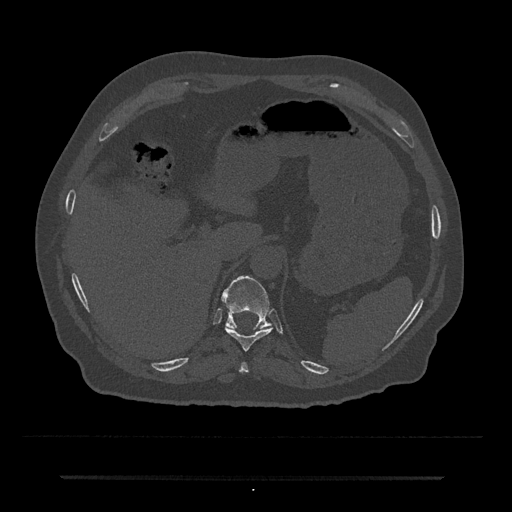
CT including the spine, one axial slice; slice 212 of 797 in the series (ordered by position); reconstruction kernel Br40s/3; bone window (W 1800 / L 400 HU); 0.5 mm slice thickness; 512 × 512 image matrix. Male patient, age 69 years. Case-level facts recorded for this patient, not image findings: primary cancer: prostate.
Annotated regions visible in this slice (semi-automatic segmentation, software-assisted and operator-edited):
- T10 vertebra: box from (x=225, y=326) to (x=273, y=351) px
- T11 vertebra: (x=221, y=275)–(x=272, y=329)
- T9 vertebra: (x=239, y=362)–(x=248, y=373)